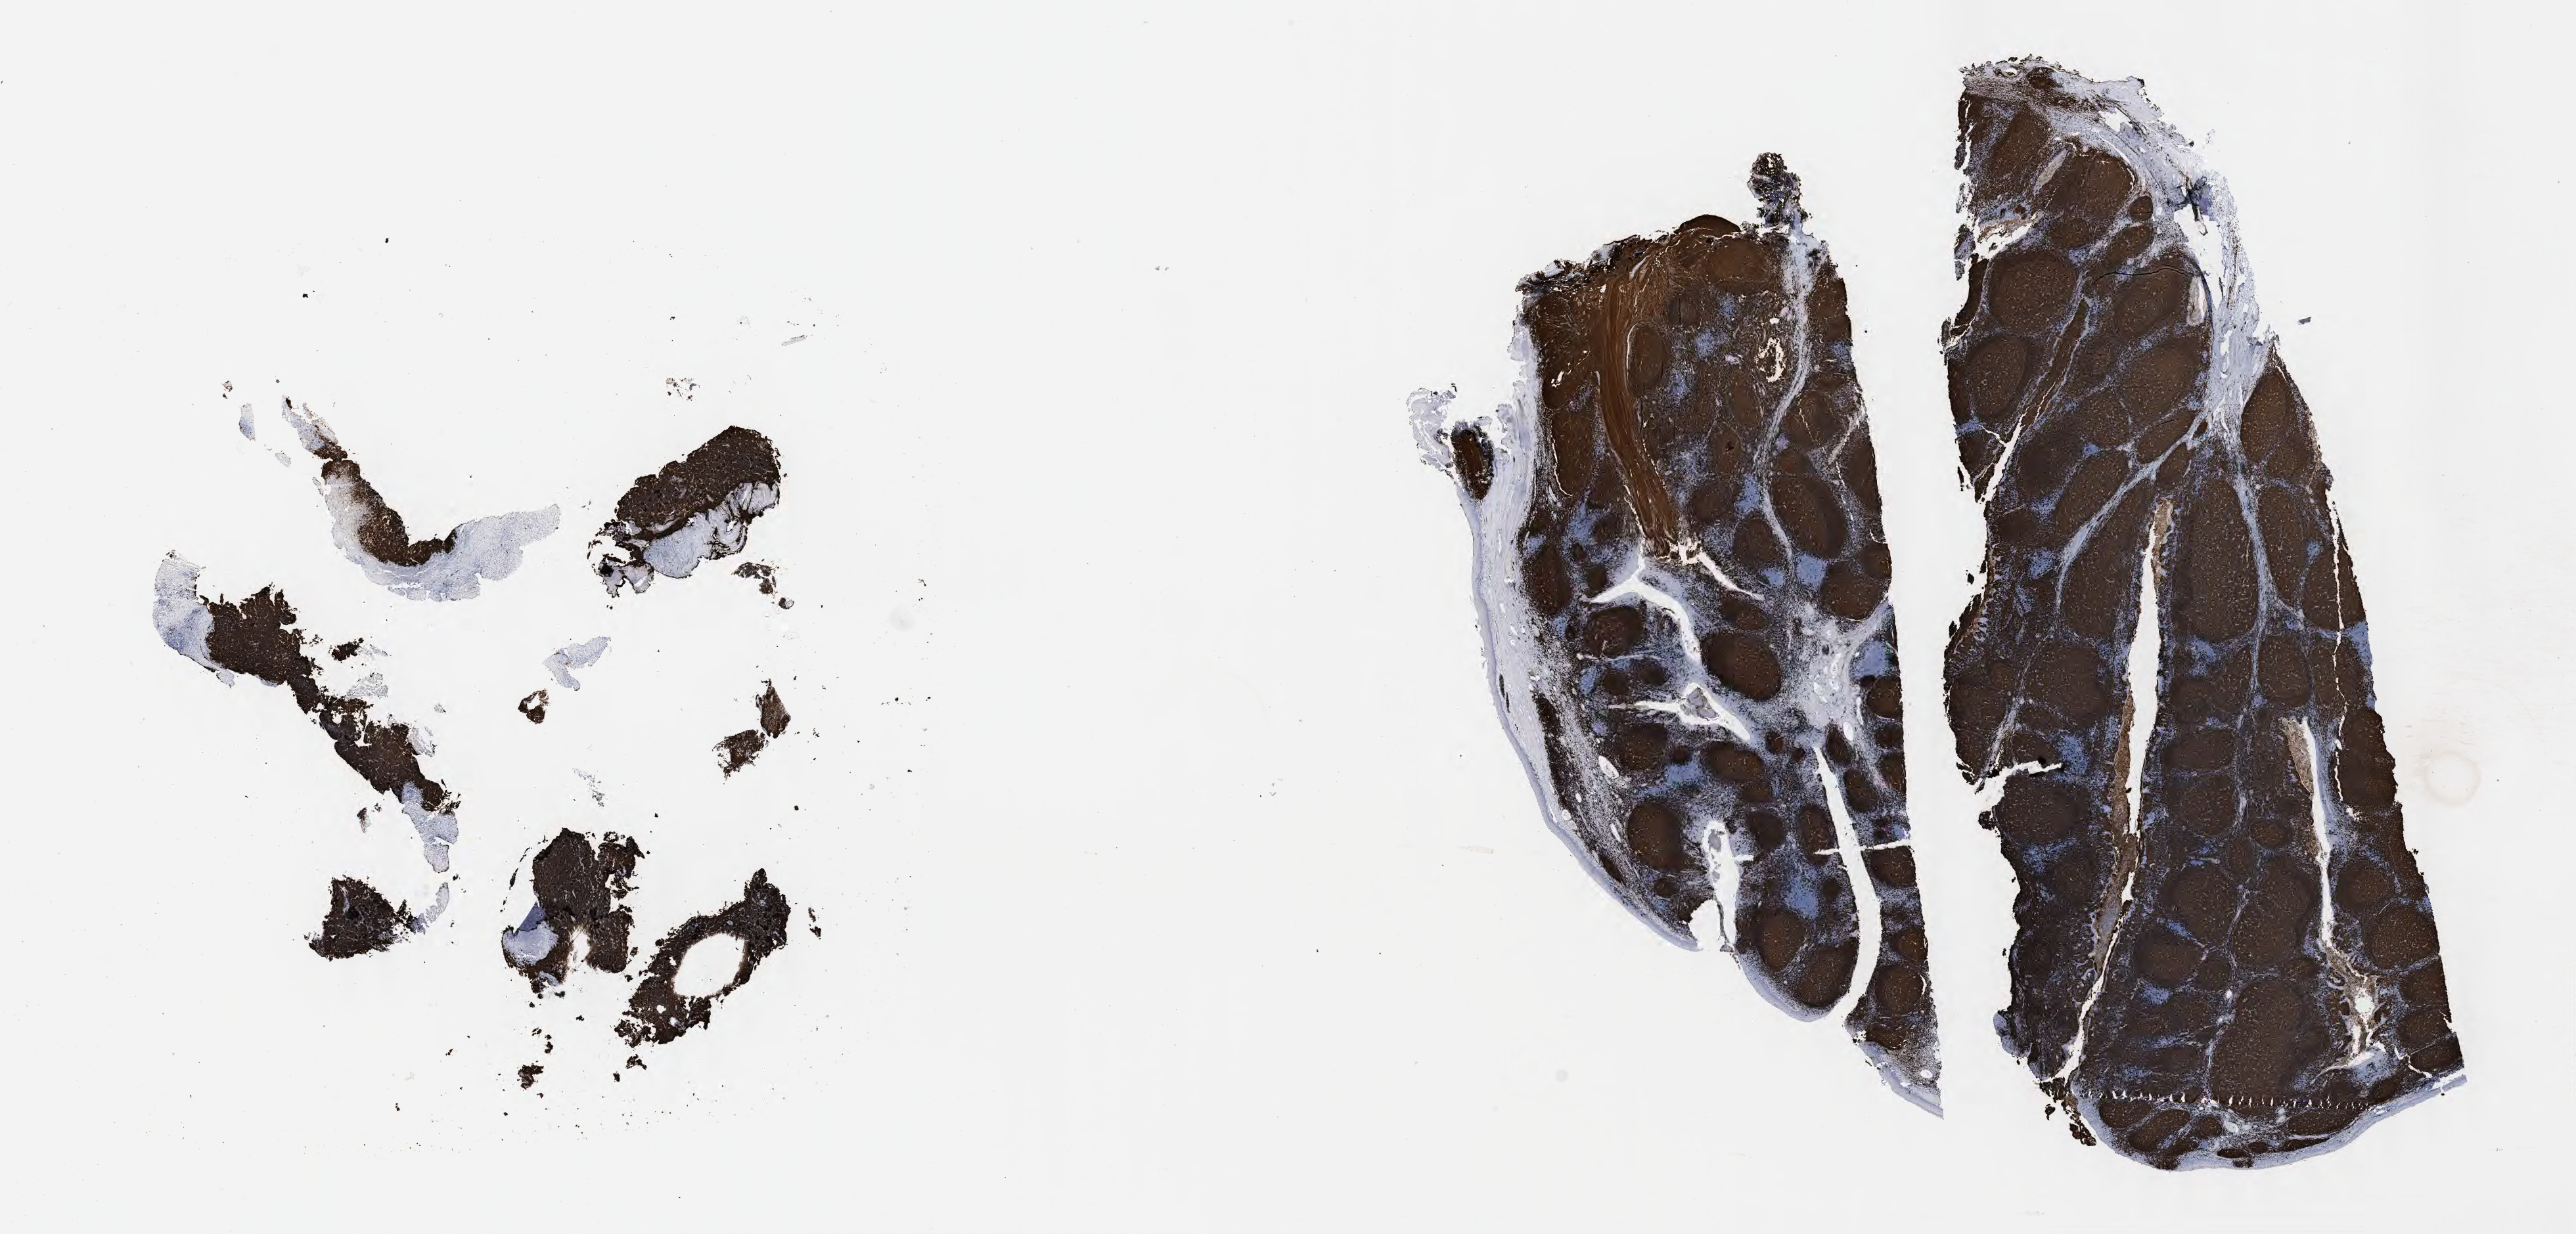
Immunohistochemistry (IHC) whole-slide image stained for CD20 — whole scanned area (about 31.7 x 15.2 mm) shown as a low-resolution overview. Specimen: tumor tissue. Female, age 9 years at initial diagnosis.
Histologic diagnosis: Burkitt lymphoma, NOS.